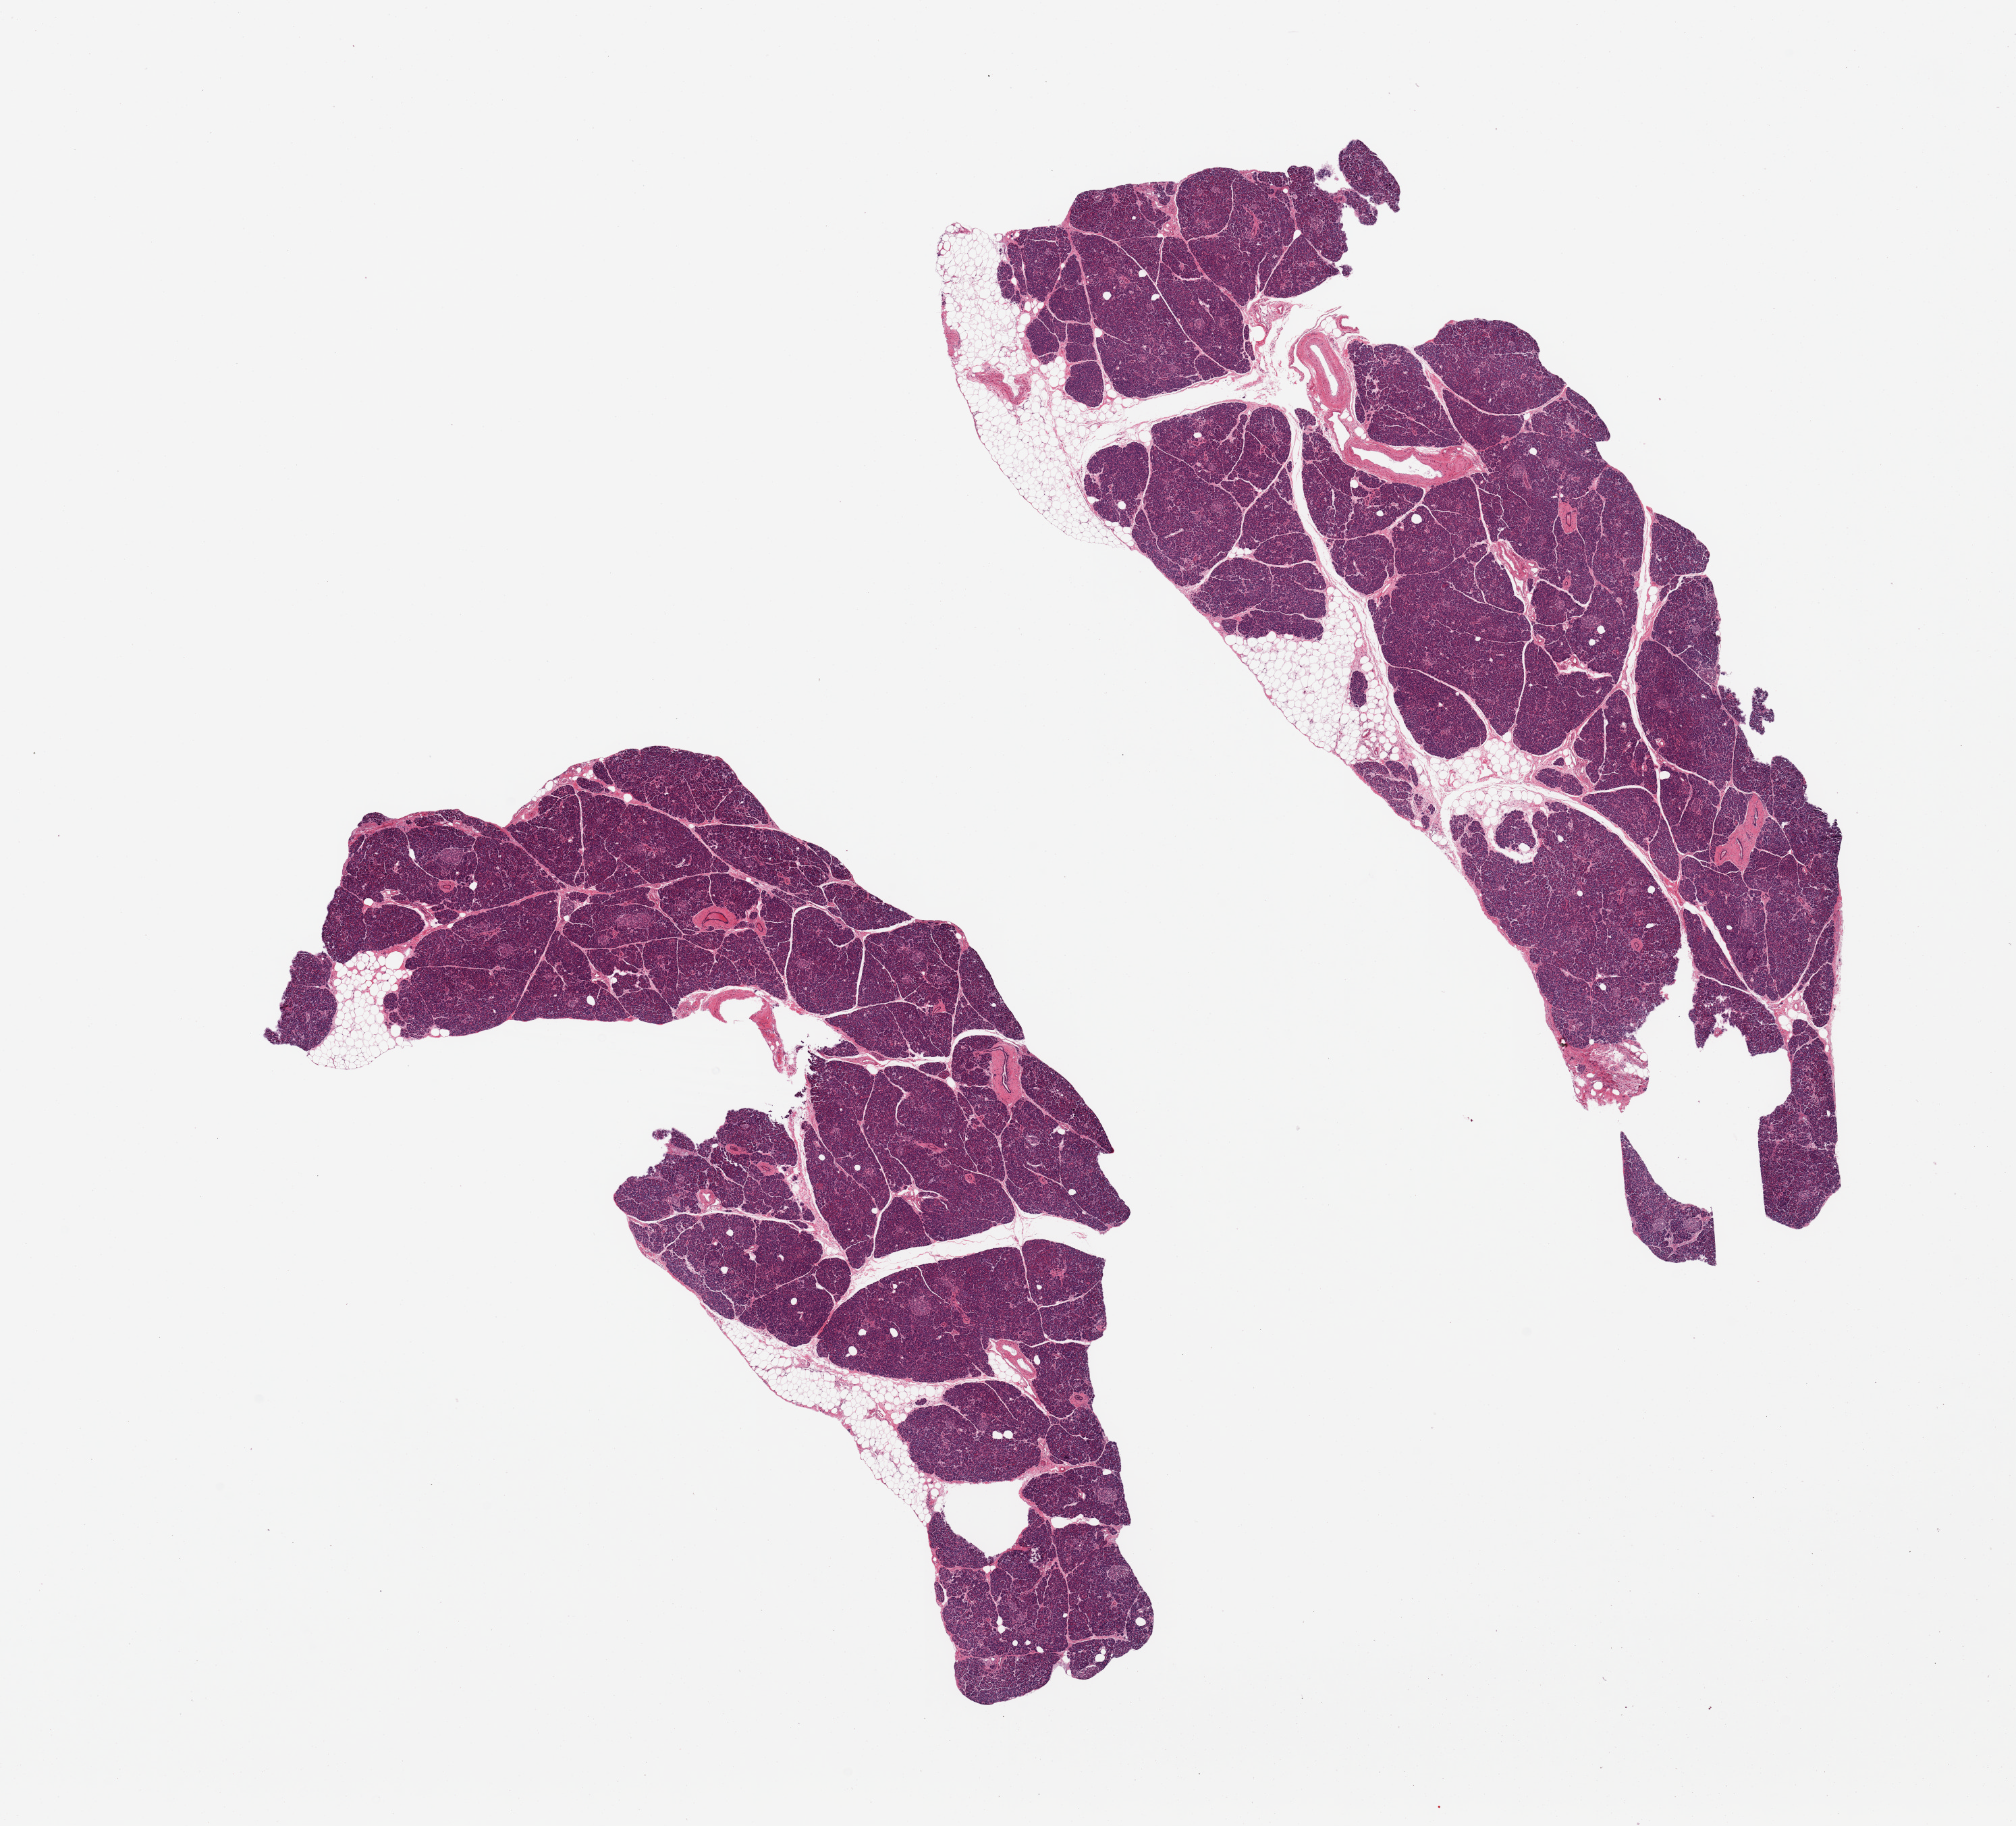
Digitized H&E-stained section — low-resolution overview of the scanned area, about 23.6 x 21.4 mm (slide scanned at 20x), PAXgene-fixed, paraffin-embedded tissue, sampled site (target tissue): pancreas, donor tissue sample. Donor sex: female.
Reviewer comment on this tissue sample: 2 pieces, remarkably well preserved, Islets well-seen.